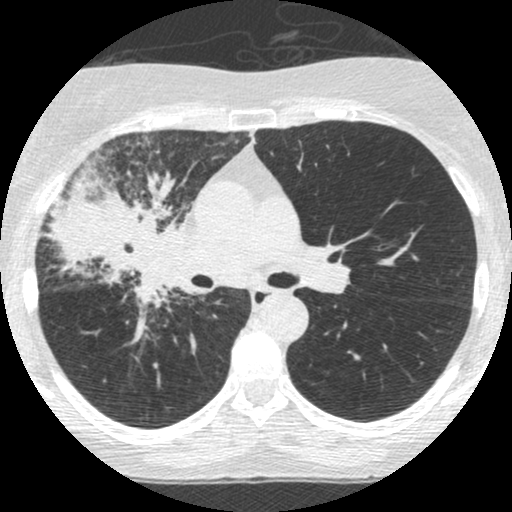
Low-dose screening chest CT, one axial slice. Position 156 of 253 along the scan axis. Lung window (W 1500 / L -600 HU). 1.25 mm slice thickness. 512 × 512 image matrix.
Structures marked on this image (manually delineated by an expert):
- lesion 2 (tumor, hilum of right lung): bounding box (x1, y1, x2, y2) in pixels: (44, 174, 183, 305)